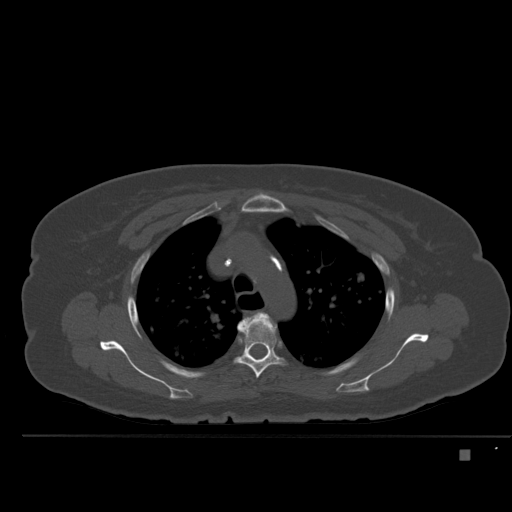
CT including the spine, one axial slice. Bone window (W 1800 / L 400 HU). 1.5 mm slice thickness. 512 × 512 image matrix, field of view 422 × 422 mm. Patient: female, 74 years. From the clinical record (not read from this slice): primary cancer: colon.
Annotated regions visible in this slice (semi-automatic segmentation, software-assisted and operator-edited):
- T3 vertebra: bounding box <238,312,277,342> (left, top, right, bottom; pixels)
- T4 vertebra: <235,316,284,378>